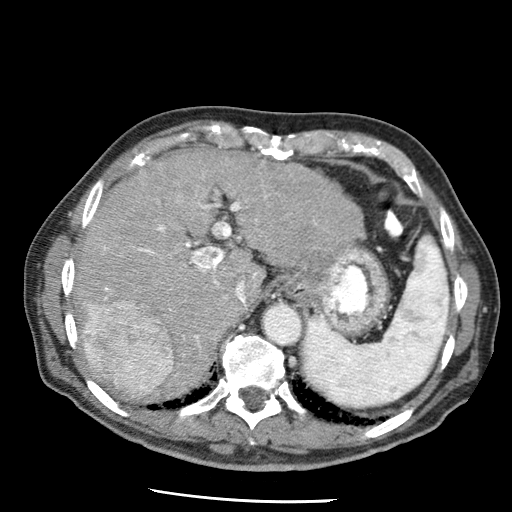
Contrast-enhanced abdominal CT (liver protocol), one axial slice. Position 47 of 79 along the scan axis. Reconstruction kernel STANDARD. Soft-tissue window (W 400 / L 40 HU). 2.5 mm slice thickness. 512 × 512 image matrix. From the clinical record (not read from this slice): diagnosis: hepatocellular carcinoma (patient treated with transarterial chemoembolisation; whether this scan precedes or follows treatment is not stated here); TNM stage (as recorded): Stage-IIIA; Child-Pugh class: A; tumour size: 7 cm.
Outlined on this slice (semi-automatically segmented with operator editing):
- liver parenchyma outside the tumour (the mass and vessels are separate outlines, so this box may not span the whole liver): box from (x=72, y=150) to (x=364, y=396) px
- mass: (x=81, y=300)–(x=173, y=397)
- liver vessels: (x=84, y=202)–(x=258, y=333)